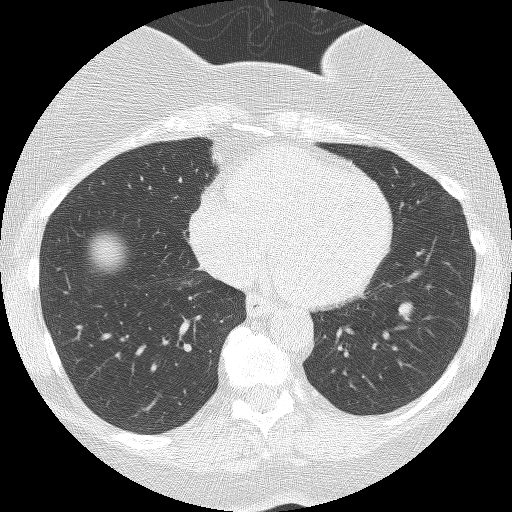
Low-dose screening chest CT, axial slice. Third annual screen. Lung window (W 1500 / L -600 HU). 120 kVp. Slice 109 of 167 in the series. 512 × 512 image matrix. Female, age 55 years at enrolment. Former smoker at enrolment.
Expert reader's lesion annotation, bounding box (x1, y1, x2, y2) in pixels: (382, 289, 430, 336). The screening reader recorded 3 non-calcified nodules or masses ≥4 mm on this exam (right lower lobe, right lower lobe, left lower lobe); which of them this box marks is not recorded. Lung cancer was diagnosed 356 days after this screen: carcinoid tumor, NOS, left lower lobe, carcinoid, stage not assessed, 10 mm at pathology.